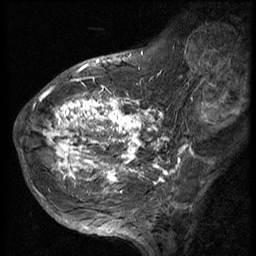
Breast MRI (dynamic contrast-enhanced), one sagittal slice. Slice 19 of 56 in the series (ordered by position). 3 images stored at this slice position (order not interpretable as contrast timing). 1.5 T. TE 4.2 ms, TR 9 ms. 2.5 mm slice thickness. 256 × 256 image matrix, field of view 180 × 180 mm. Patient: female, 49 years. From the clinical record (not read from this slice): setting: breast cancer imaged before/during neoadjuvant chemotherapy; receptor status: HER2-positive.
Structures marked on this image (semi-automatically segmented with operator editing):
- analysis volume of interest (the breast-tissue region the enhancement analysis was run in; not a lesion): bounding box <37,85,145,207> (left, top, right, bottom; pixels)
- tumour enhancement mask (voxels above the 140 % enhancement threshold inside the analysis volume of interest): <38,87,145,203>